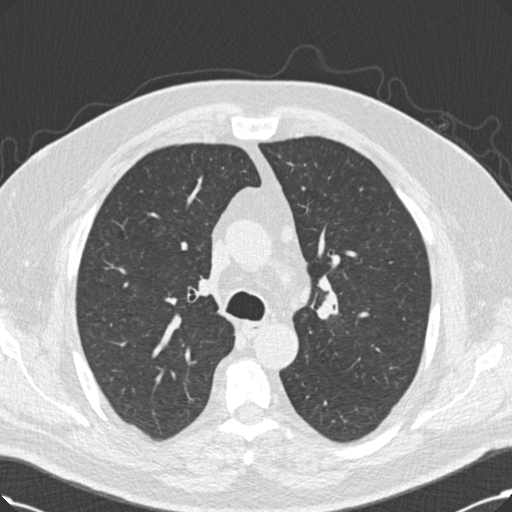
Low-dose screening chest CT, axial slice; third annual screen; lung window (W 1500 / L -600 HU); 2 mm slice thickness; standard (soft-tissue) reconstruction kernel (B30f); 120 kVp; slice 64 of 214 in the series. Male, age 60 years at enrolment. Current smoker at enrolment.
• Expert reader's lesion annotation, bounding box (x1, y1, x2, y2) in pixels: (316, 290, 348, 327).
• The exam's reader record, not a measurement of the box and not confirmed to be the same lesion: non-calcified nodule or mass ≥4 mm, left upper lobe, 20 × 20 mm, smooth margins, soft tissue attenuation, pre-existing on the prior screen: no.
• Official screen result: positive, other.
• Lung cancer was diagnosed 53 days after this screen: squamous cell carcinoma, NOS, right upper lobe, 27 mm at pathology.